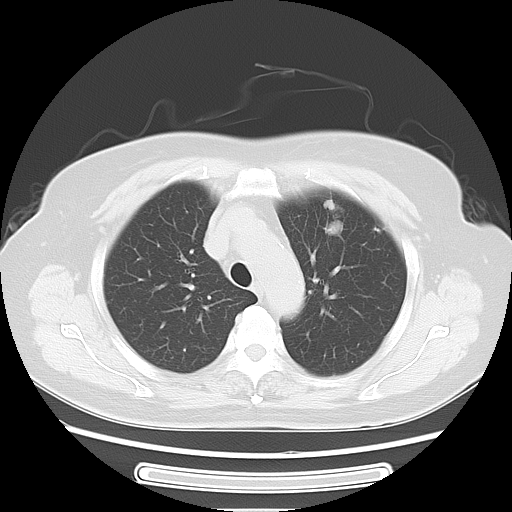
Chest CT, one axial slice. Slice 45 of 57 in the series (ordered by position). Reconstruction kernel LUNG. 120 kVp. Lung window (W 1500 / L -600 HU). 5 mm slice thickness. 512 × 512 image matrix, field of view 363 × 363 mm. Patient: female, 77 years. From the clinical record (not read from this slice): clinical TNM (as recorded): T1c N3 M0; histopathological grade: G2-3.
Annotated regions visible in this slice (bounding box drawn by a radiologist):
- lung tumour (recorded histology: adenocarcinoma): bounding box <310,189,357,248> (left, top, right, bottom; pixels)